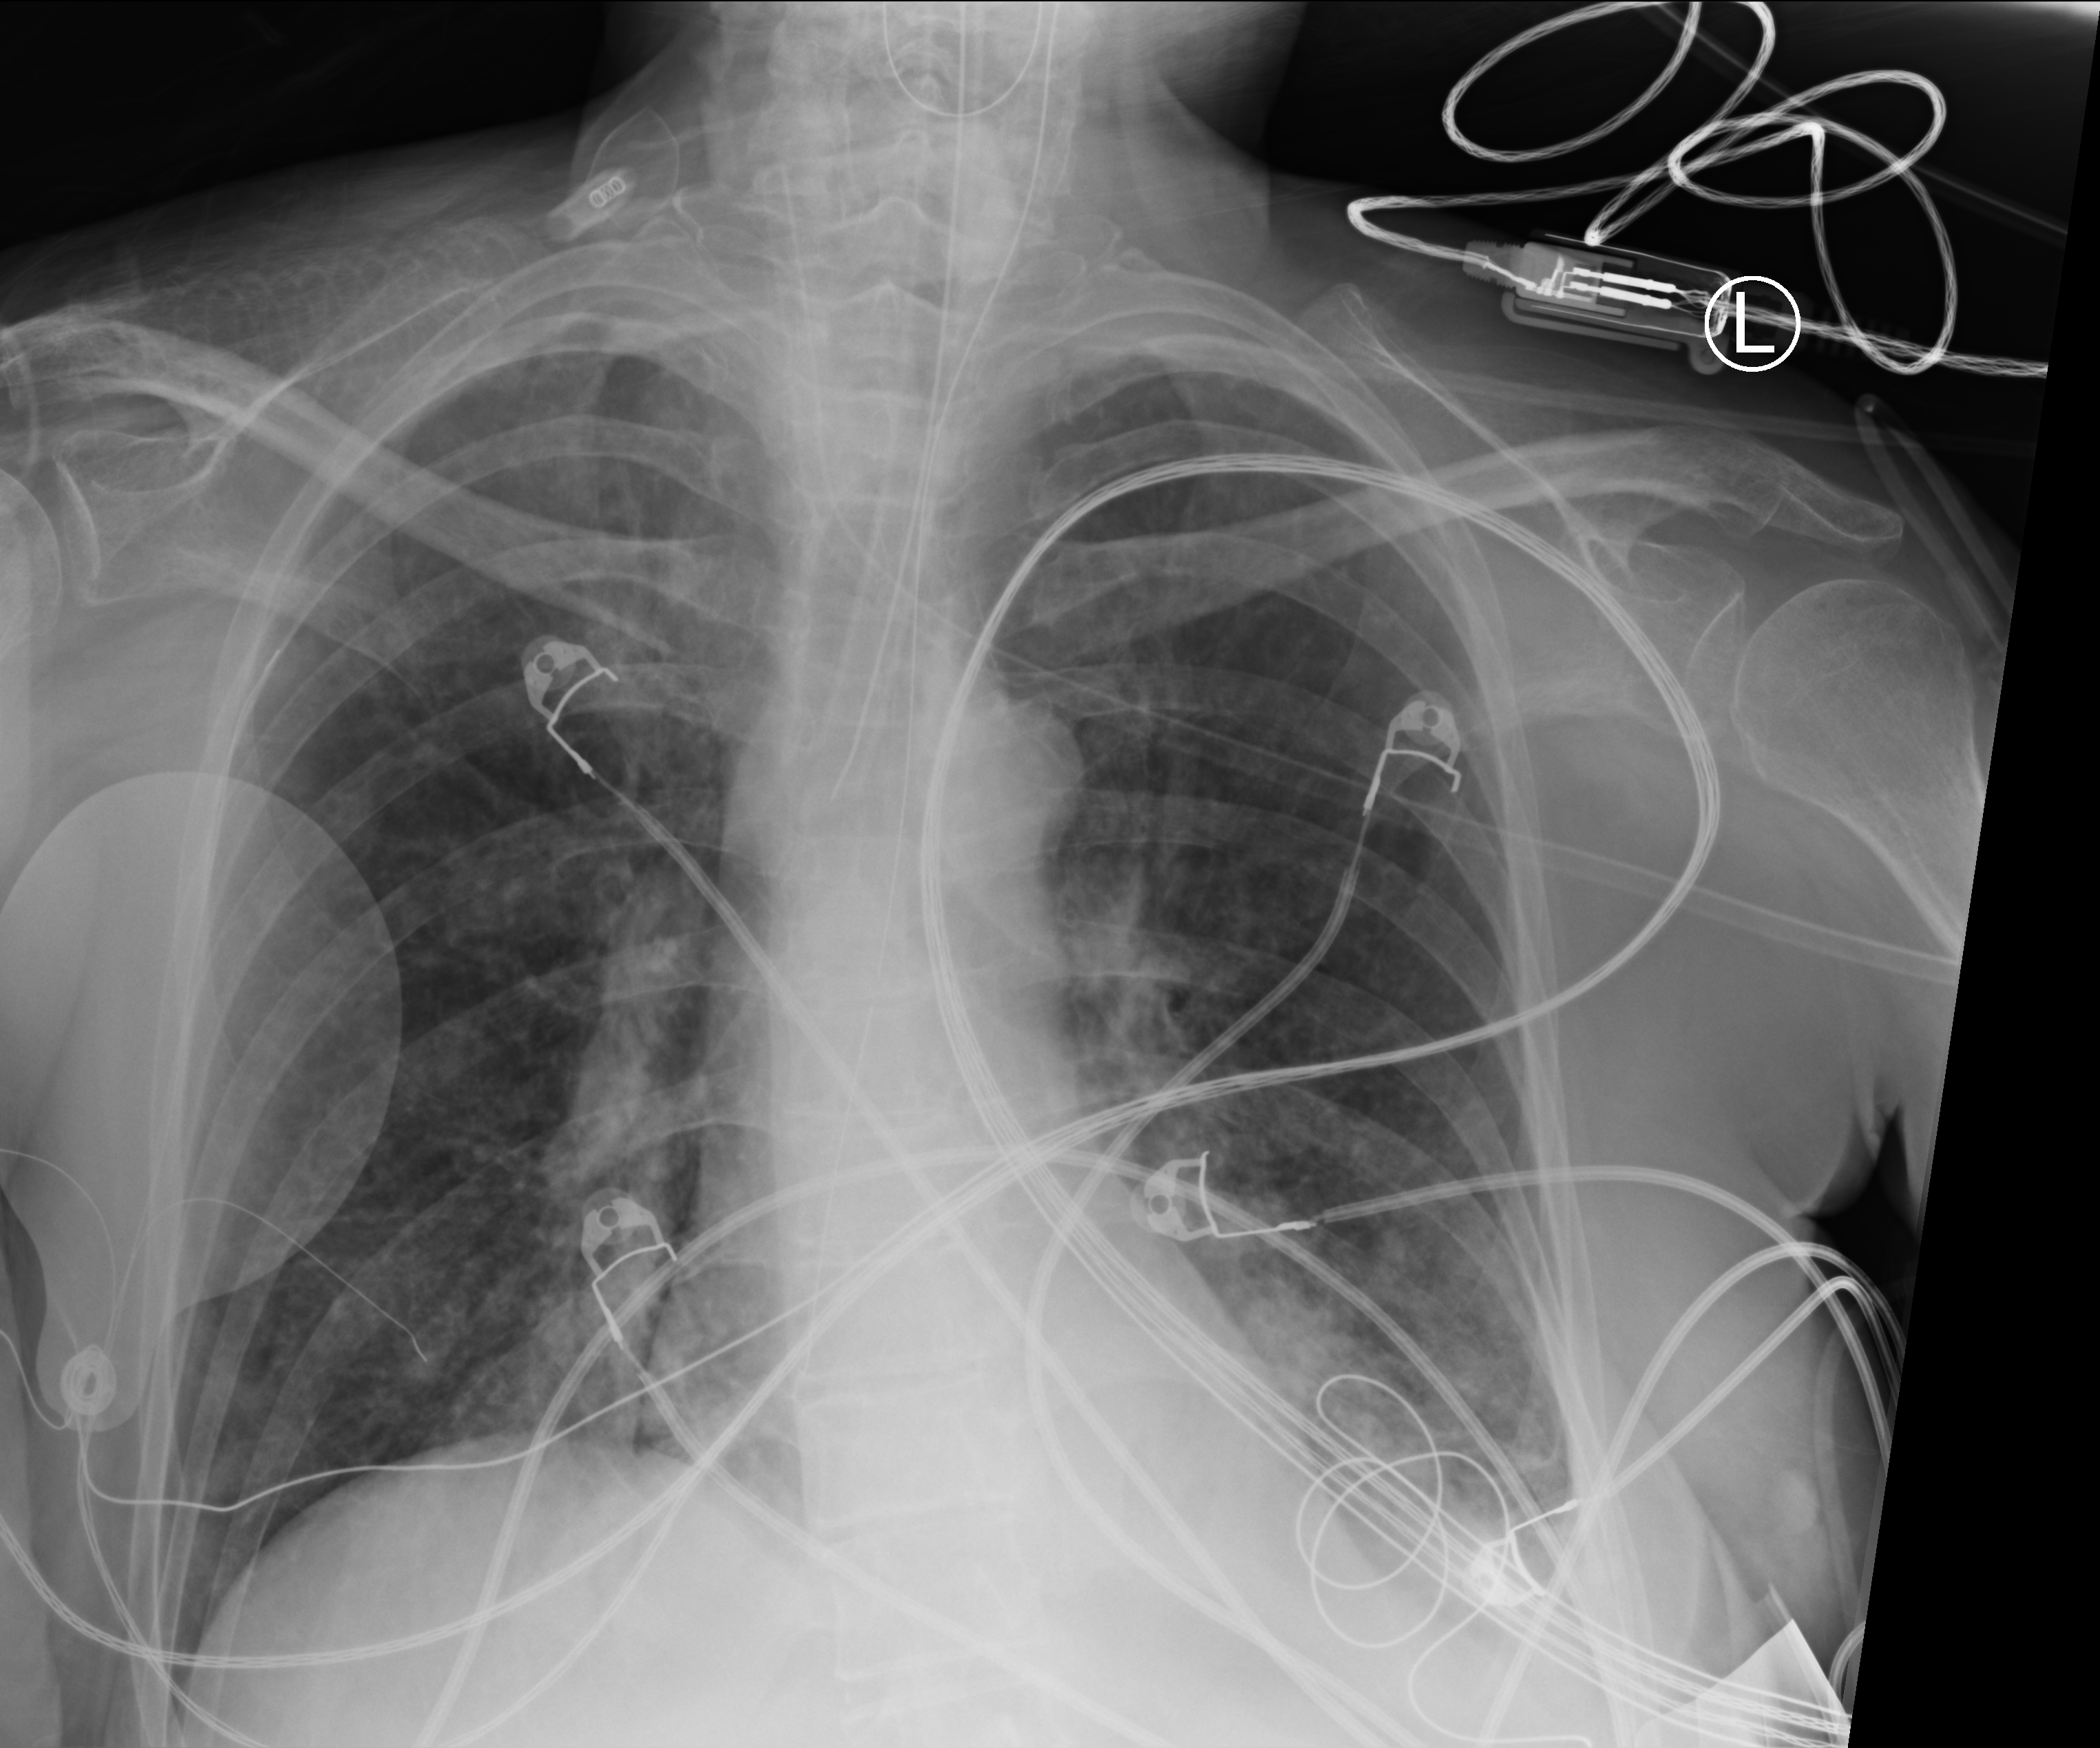
Bedside chest radiograph (computed radiography). Adult patient hospitalised with COVID-19, age 18–59 years.
Admission-level facts for this patient (not findings on this image; timing relative to this image not recorded):
- admitted to intensive care during this hospital stay: yes
- mechanically ventilated during this hospital stay: yes